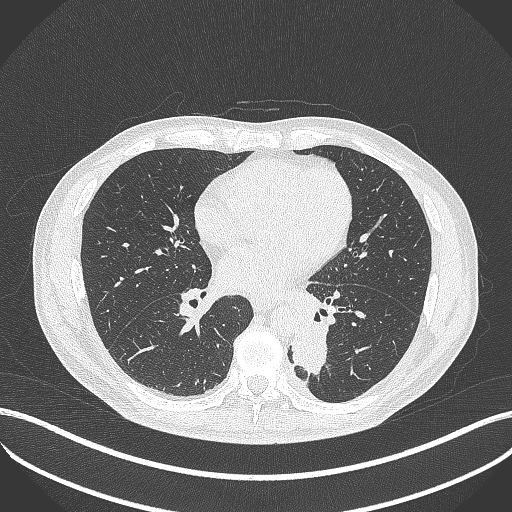
Chest CT, one axial slice. Position 181 of 451 along the scan axis. Reconstruction kernel B70f. 120 kVp. Lung window (W 1500 / L -600 HU). 1 mm slice thickness. 512 × 512 image matrix. Patient: male, 72 years. Case-level facts recorded for this patient, not image findings: clinical TNM (as recorded): T2b N0 M1.
Annotated regions visible in this slice (rectangle marked by the reading radiologist):
- lung tumour (recorded histology: adenocarcinoma): bounding box [x1, y1, x2, y2] px = [291, 314, 330, 382]